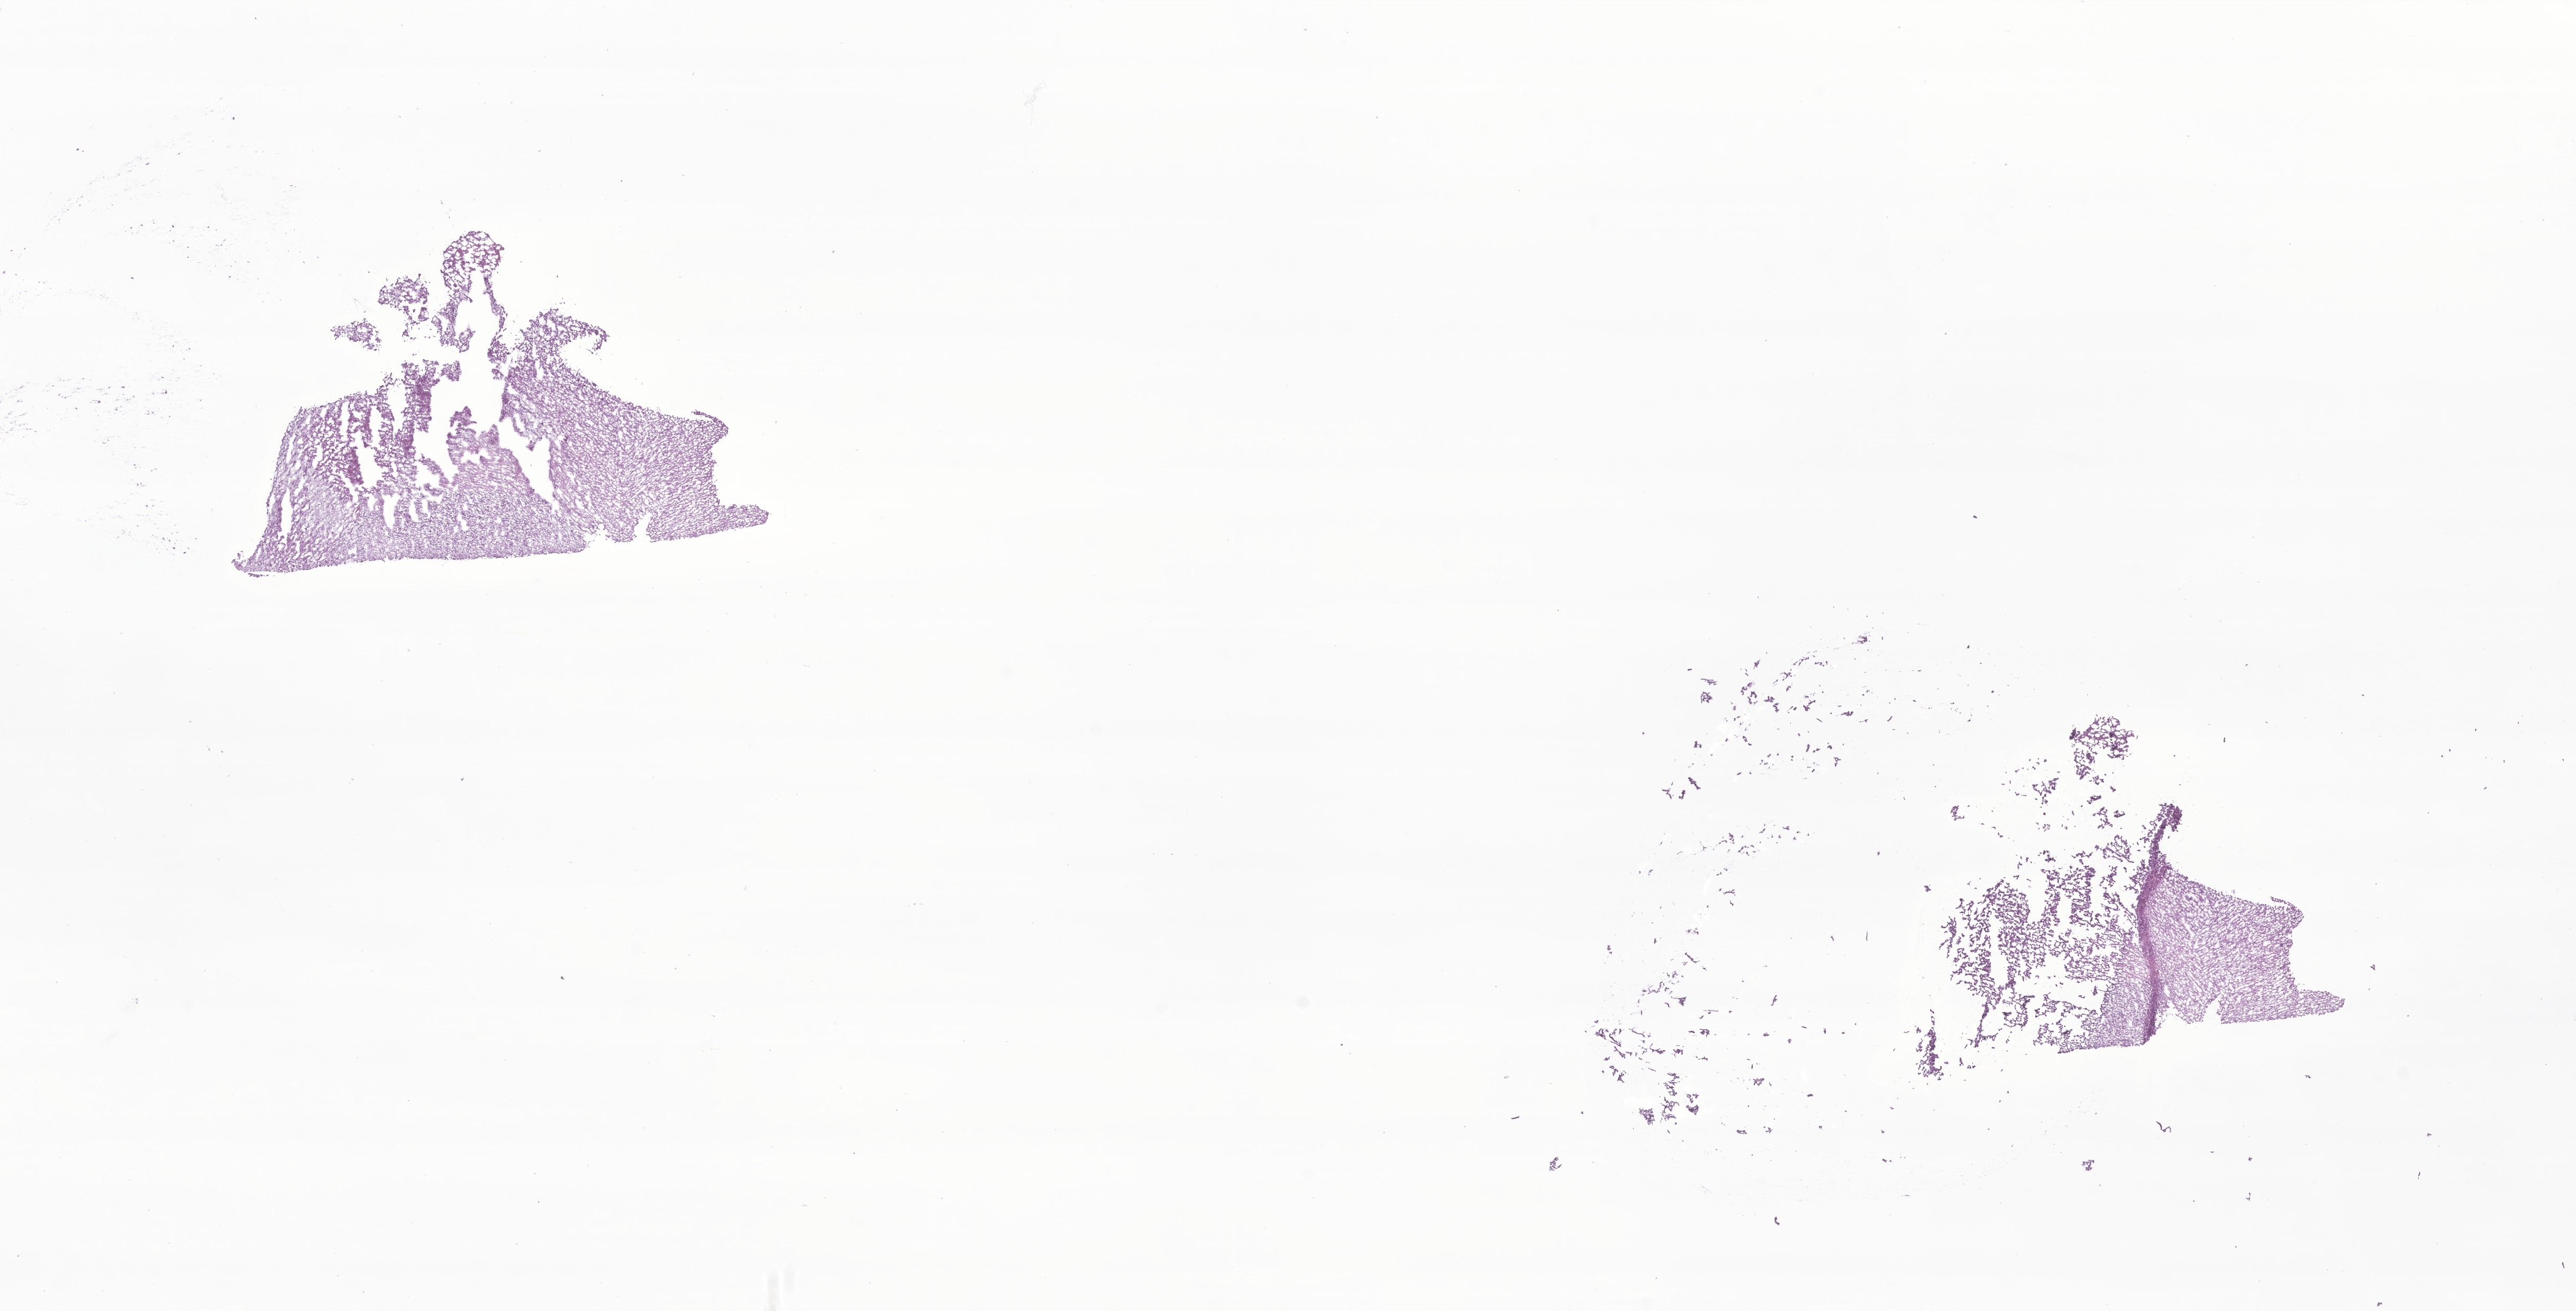
Digitized hematoxylin and eosin (H&E)-stained section of tumor tissue from the brain — a low-resolution overview of the entire scanned area, about 20.5 x 10.4 mm; frozen section (OCT-embedded). Female patient, age 210 months.
Diagnosis (ICD-O-3 morphology term): Neoplasm, uncertain whether benign or malignant.